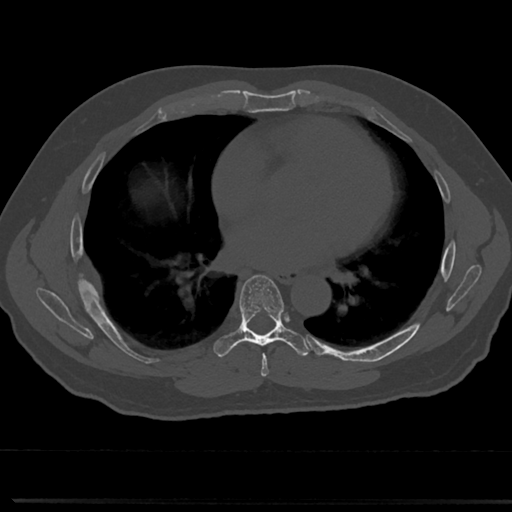
CT including the spine, one axial slice. Slice 412 of 817 in the series (ordered by position). Reconstruction kernel Br40s/3. 120 kVp. Bone window (W 1800 / L 400 HU). 0.5 mm slice thickness. 512 × 512 image matrix, field of view 355 × 355 mm. Male patient, age 61 years. From the clinical record (not read from this slice): primary cancer: prostate.
Outlined on this slice (semi-automatically segmented with operator editing):
- T6 vertebra: bounding box [x1, y1, x2, y2] px = [252, 336, 319, 367]
- T7 vertebra: [217, 274, 305, 356]